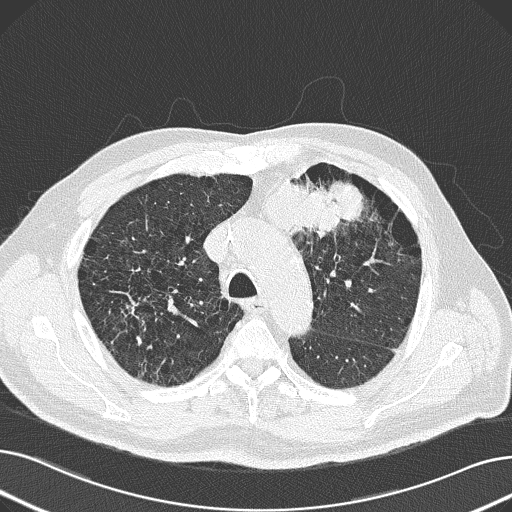
Axial slice from a low-dose chest CT screening exam; baseline screening round; lung window (W 1500 / L -600 HU); slice 54 of 165 in the series. Male participant, aged 69 years at enrolment.
Expert reader's lesion annotation, box from (x=226, y=149) to (x=379, y=255) px. Reader record for this screening exam (exam-level; its link to the box is not recorded): non-calcified nodule or mass ≥4 mm, left upper lobe, 6 × 10 mm, spiculated (stellate) margins, soft tissue attenuation. Official screen result: positive, change unspecified: nodule(s) >= 4 mm or enlarging nodule(s), mass(es), or other non-specific abnormalities suspicious for lung cancer. Lung cancer was diagnosed 20 days after this screen: non-small cell carcinoma, left upper lobe, poorly differentiated (G3), stage IB (AJCC 6th edition), 100 mm at pathology.